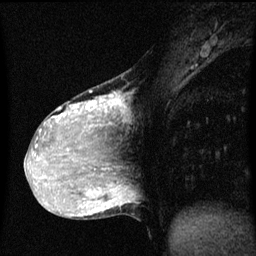
Breast MRI (dynamic contrast-enhanced), one sagittal slice; slice 24 of 60 in the series (ordered by position); dynamic contrast-enhanced series, image 2 of 3 at this slice position (ordered by acquisition); 1.5 T; TE 4.2 ms, TR 8 ms; 2 mm slice thickness; 256 × 256 image matrix, field of view 200 × 200 mm. Female patient, age 36 years.
Annotated regions visible in this slice (semi-automatically segmented with operator editing):
- analysis volume of interest (the breast-tissue region the enhancement analysis was run in; not a lesion): bounding box (x1, y1, x2, y2) in pixels: (33, 72, 129, 169)
- tumour enhancement mask (voxels above the 70 % enhancement threshold inside the analysis volume of interest): (33, 92, 120, 169)